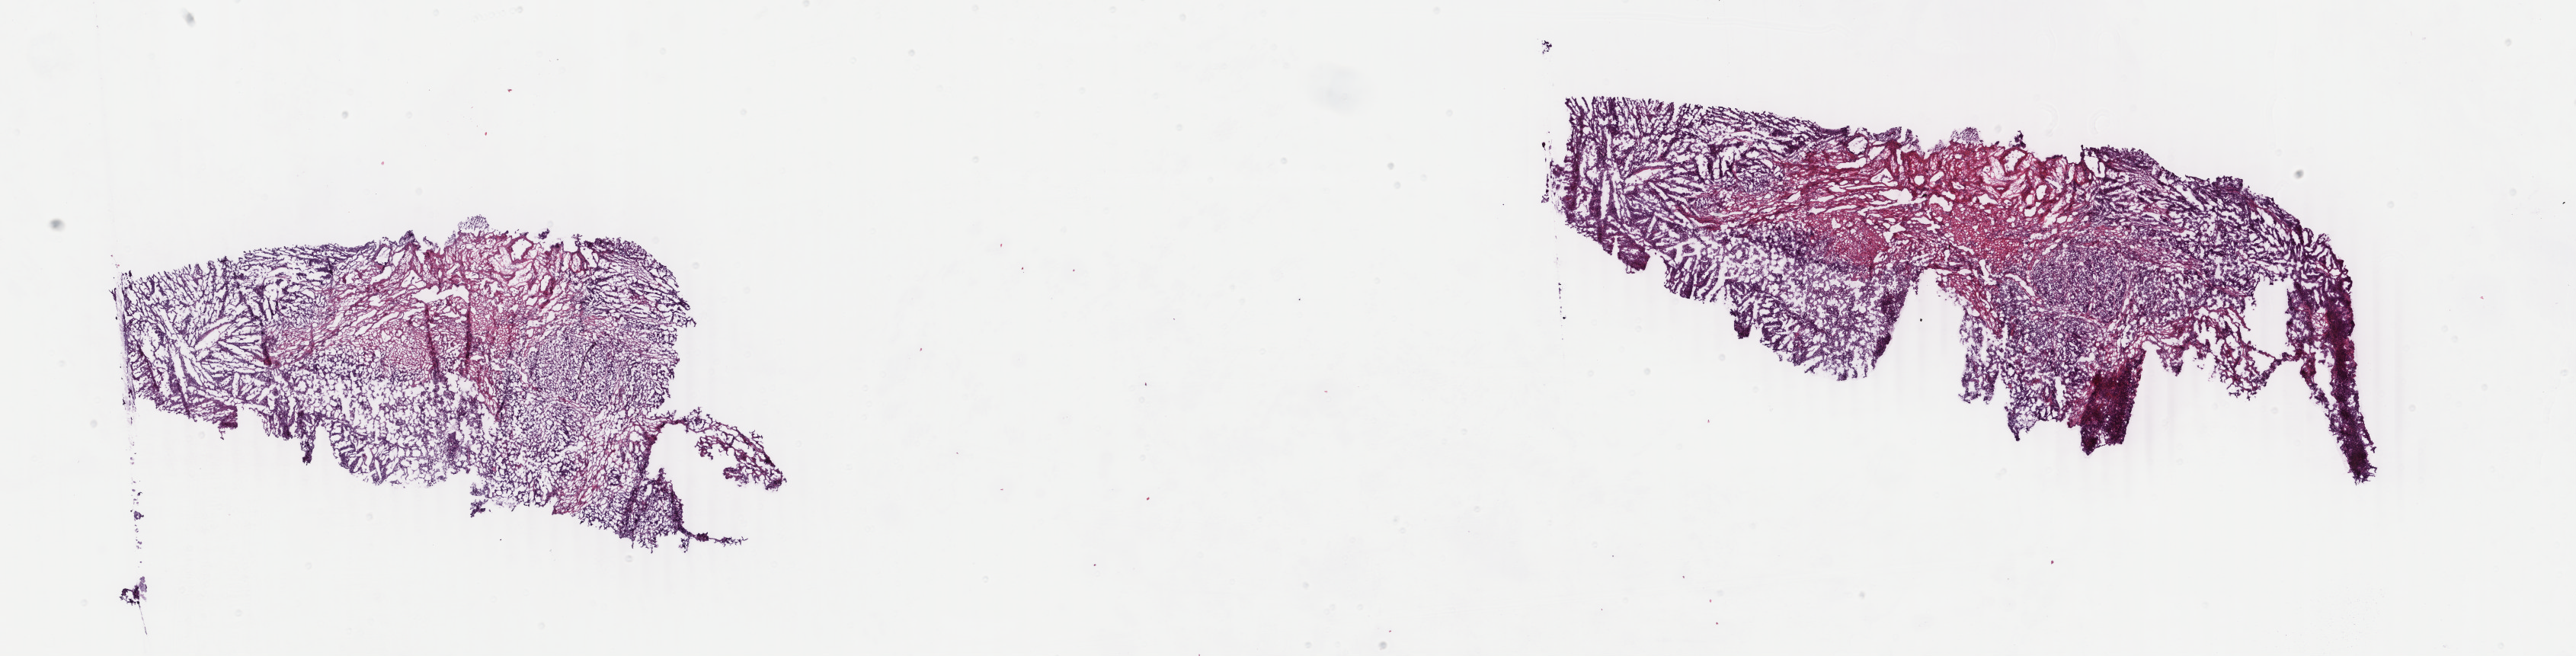
Whole-slide histology image, H&E — a low-resolution overview of the entire scanned area, about 26.9 x 6.8 mm, frozen section from the top of the tissue portion, primary tumour sample from the uterus. Patient: female, age at initial diagnosis 80 years. Histologic grade: G2 (moderately differentiated). Composition of this section per pathologist review: tumour cells 64%, tumour nuclei 70%, normal cells 30%, stromal cells 5%, necrosis 1%. Infiltration values recorded for this section: lymphocyte infiltration 0%, monocyte infiltration 0%, neutrophil infiltration 0%.
Lymph nodes positive (case pathology): 0 of 7 examined. FIGO stage: IB. Diagnosis: Endometrioid adenocarcinoma, NOS (endometrium).